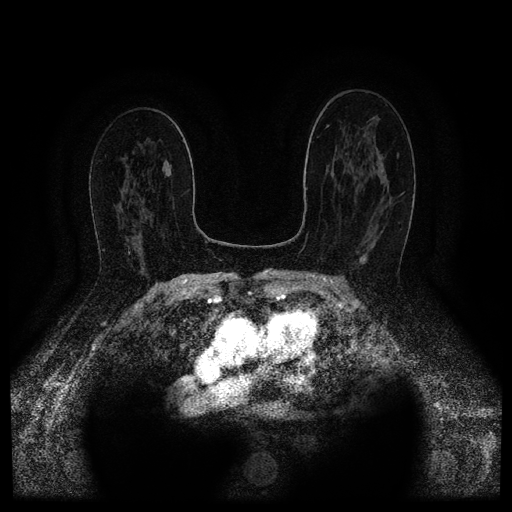
Breast MRI (dynamic contrast-enhanced, multi-phase), one axial slice; position 63 of 116 along the scan axis; dynamic contrast-enhanced series, time point 2 of 5 at this slice position (early post-contrast); 1.5 T; TE 2.6 ms, TR 5.4 ms; 512 × 512 image matrix, field of view 340 × 340 mm. Female patient, age 67 years.
Structures marked on this image (semi-automatically segmented with operator editing):
- breast lesion (labelled 'tumour' in the annotation; benign lesions carry a separate 'benign' label): box from (x=359, y=243) to (x=376, y=265) px